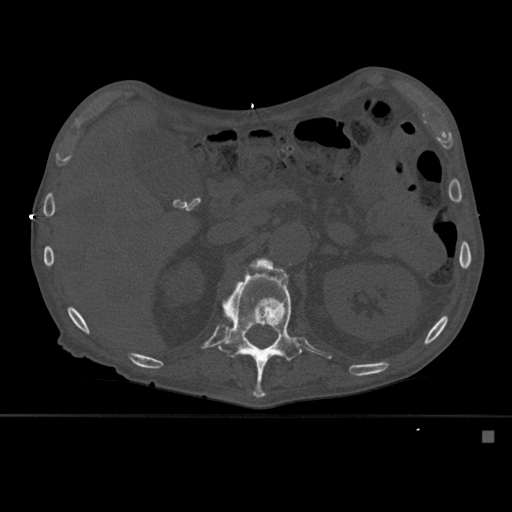
CT including the spine, one axial slice. Position 258 of 527 along the scan axis. Bone window (W 1800 / L 400 HU). 512 × 512 image matrix. Male patient, age 78 years. From the clinical record (not read from this slice): primary cancer: prostate.
Outlined on this slice (semi-automatically segmented with operator editing):
- L1 vertebra: box from (x=219, y=258) to (x=302, y=398) px